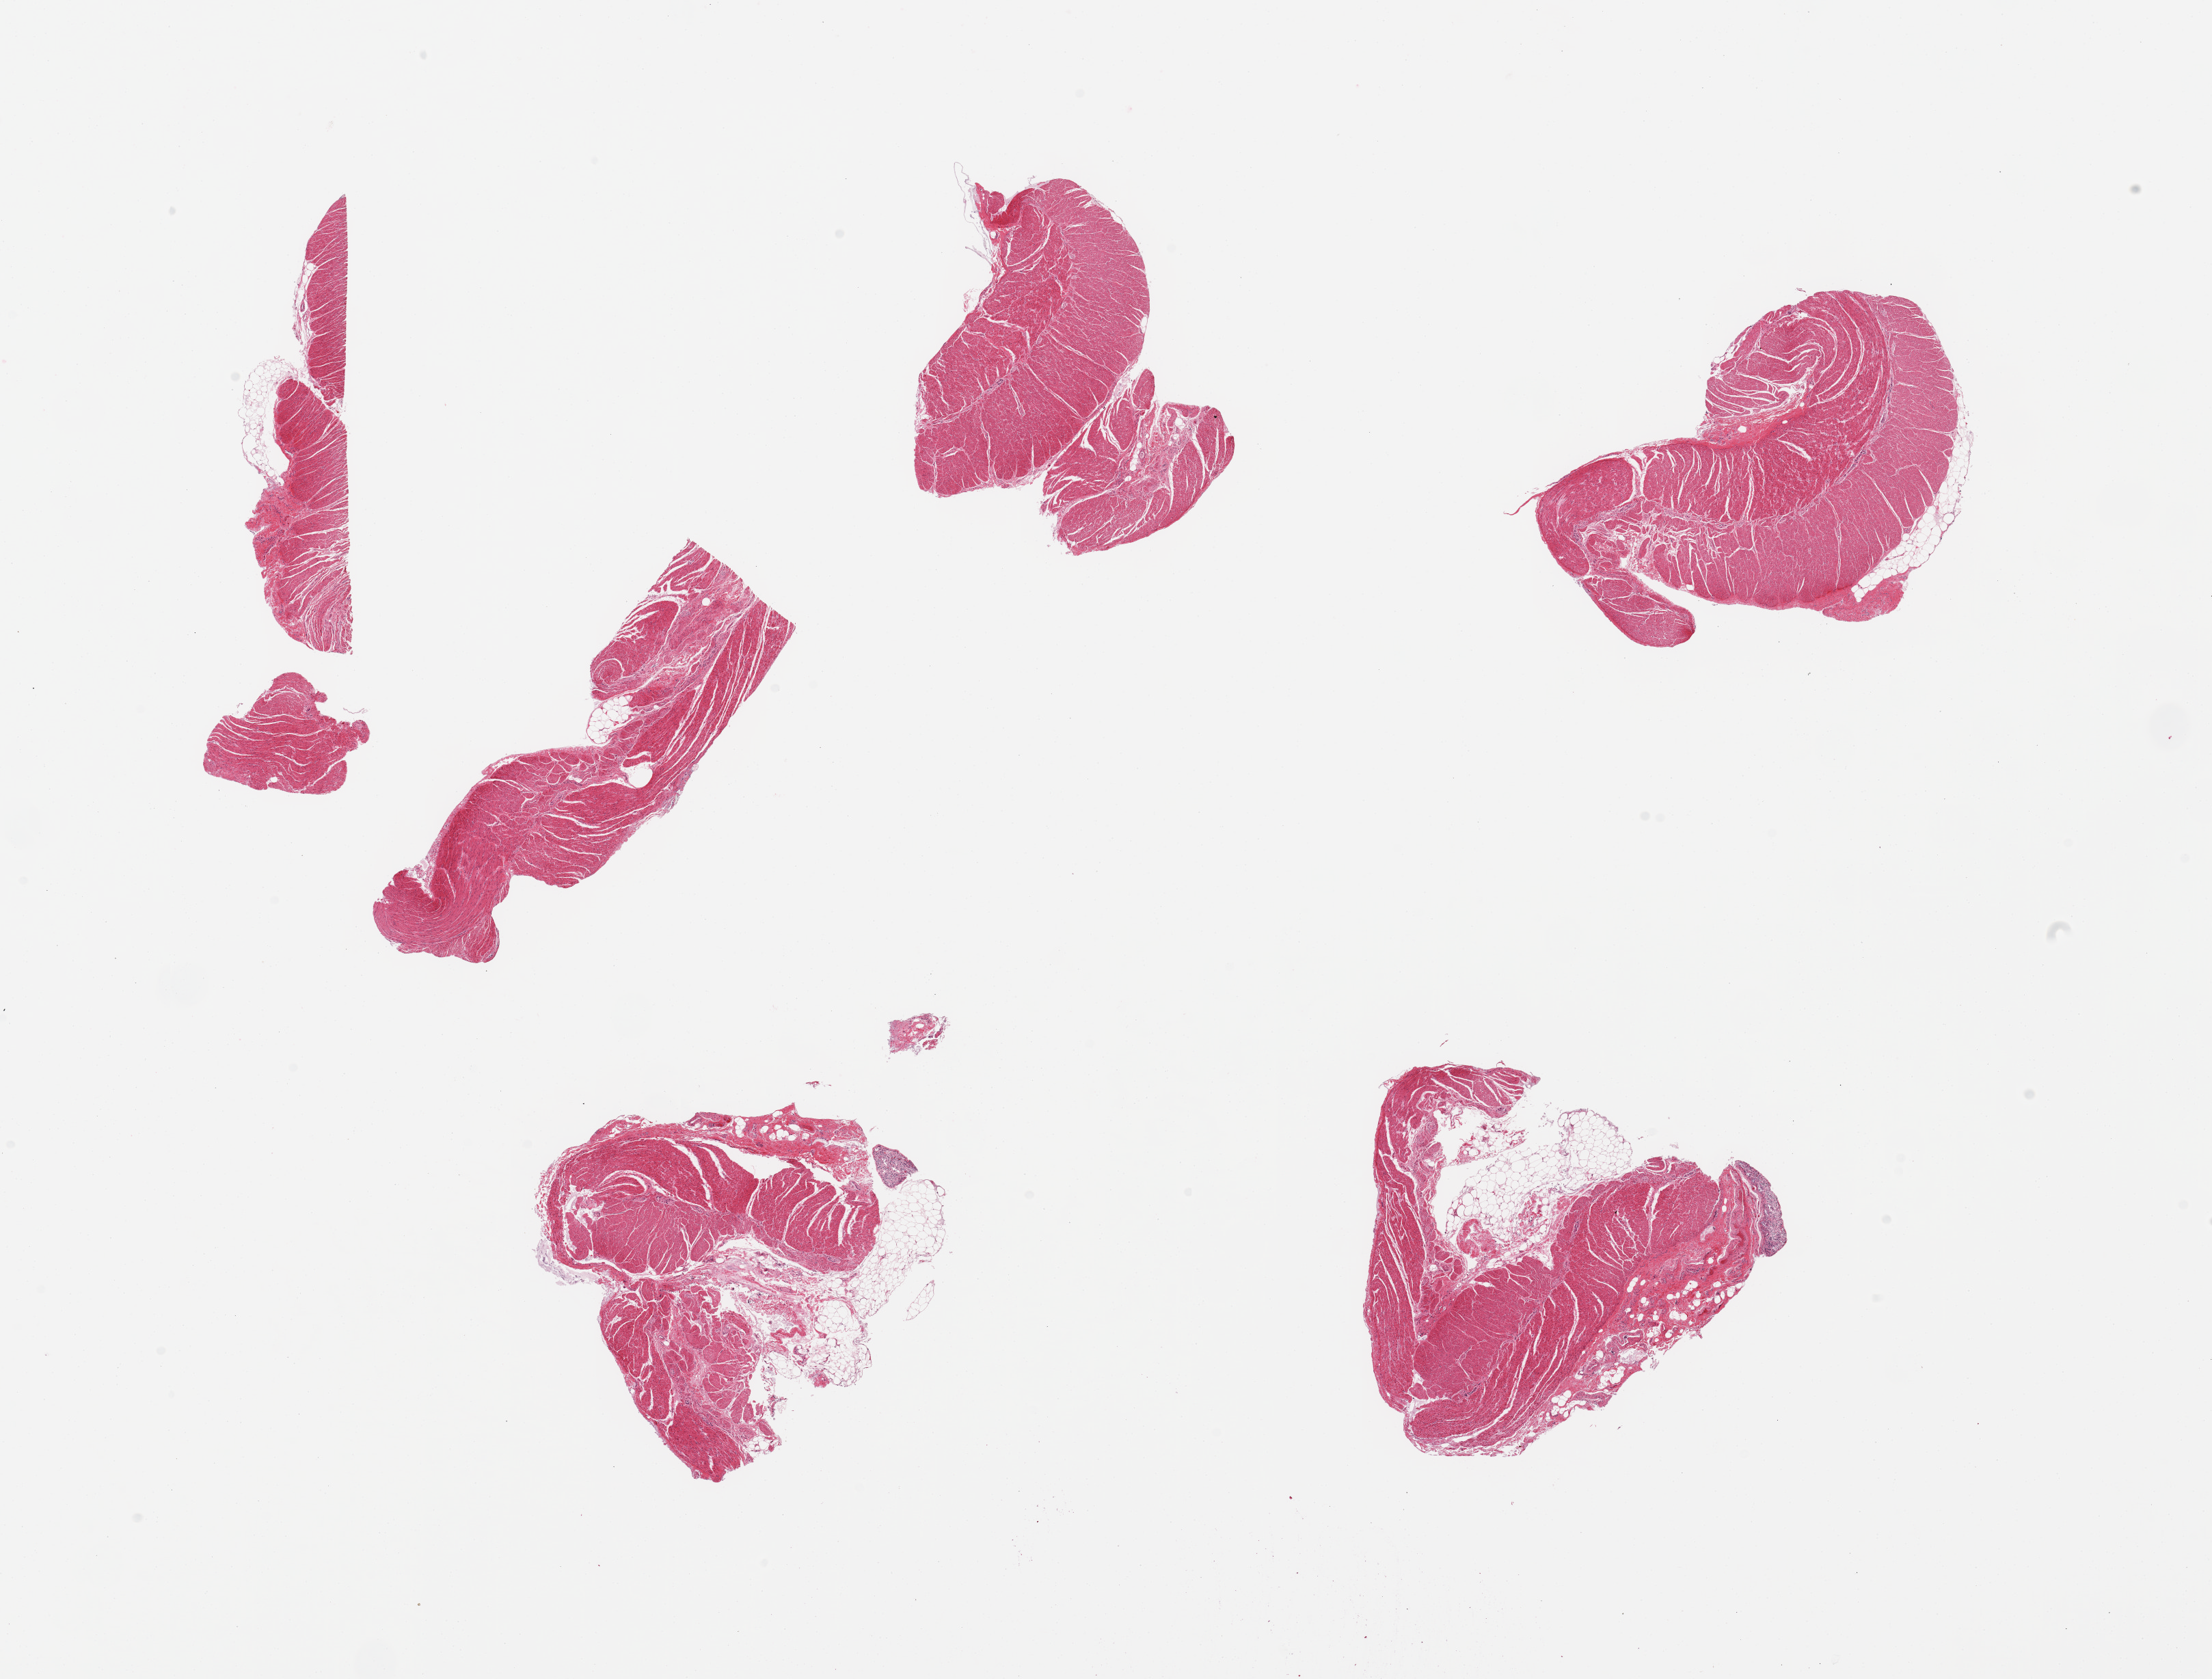
Digitized hematoxylin and eosin (H&E)-stained section — whole scanned area (about 25.6 x 19.4 mm, from a 20x scan) shown as a low-resolution overview, PAXgene-fixed, paraffin-embedded tissue, sampled site (target tissue): sigmoid colon, tissue donor sample.
Reviewer comment on this tissue sample: 6 pieces (fragmented); predominantly muscularis with few strips of residual autolyzed mucosa; 2 pieces with ~10% attached fat.